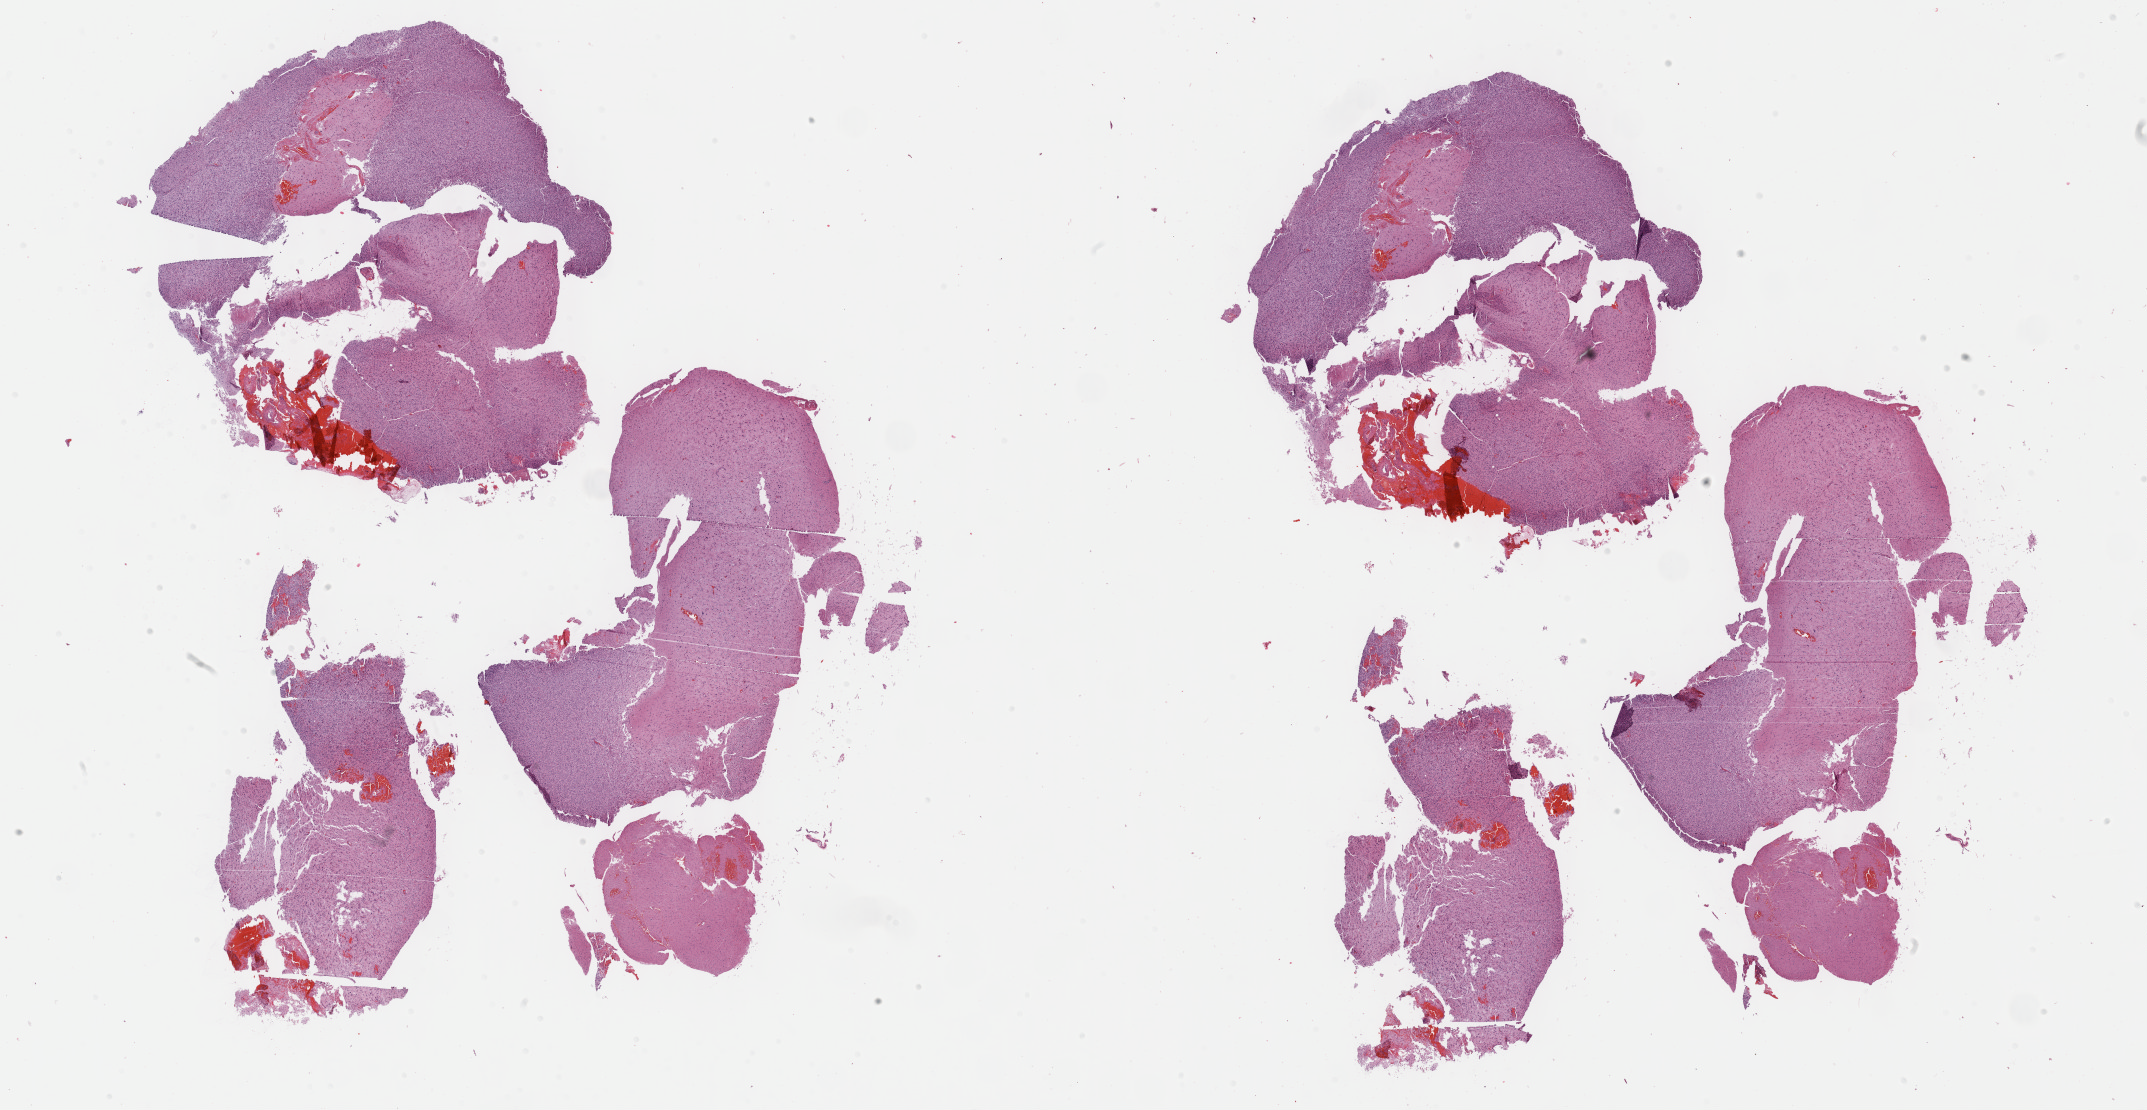
H&E-stained whole-slide image — low-resolution overview of the scanned area, about 34.7 x 18.0 mm (from a 40x scan). Formalin-fixed paraffin-embedded (FFPE) diagnostic section. Sample: primary tumour, brain. Female, age 61 years at initial diagnosis. Histologic grade: G3 (poorly differentiated).
Pathologic diagnosis: Astrocytoma, anaplastic (cerebrum).